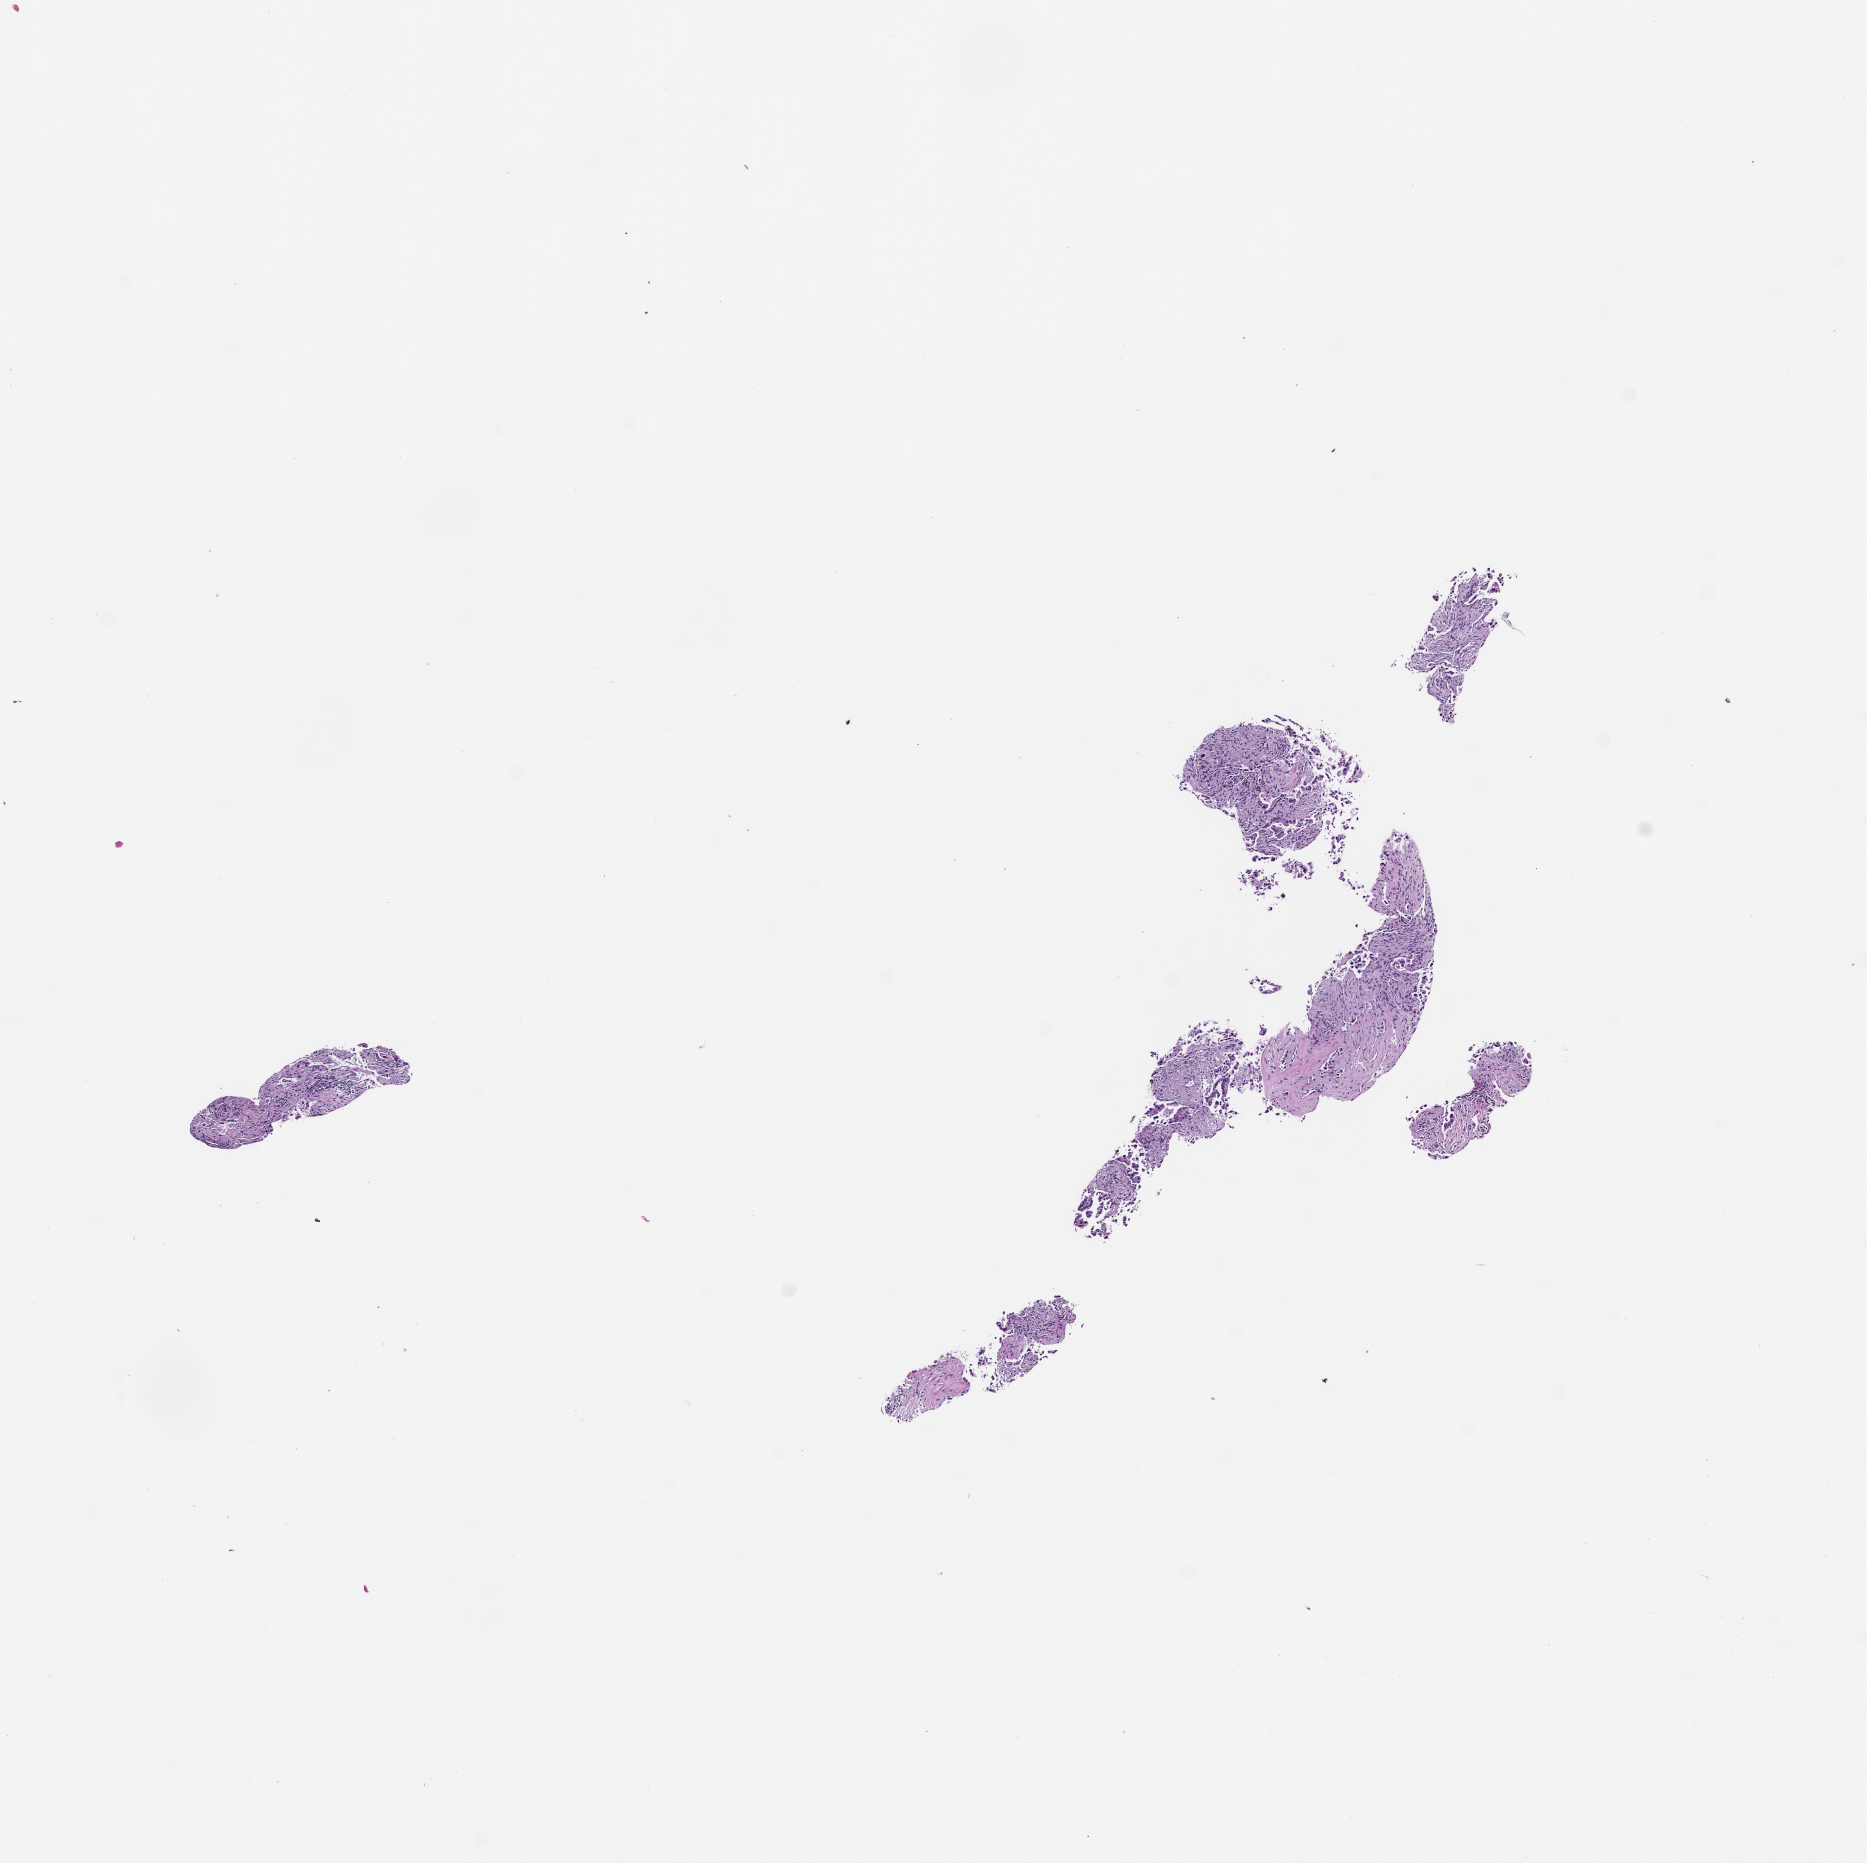
Hematoxylin and eosin (H&E) whole-slide image, whole scanned area (about 7.5 x 7.5 mm) shown as a low-resolution overview, formalin-fixed paraffin-embedded section, site: lung, collected at baseline (before treatment). Female patient.
* this section: primary tumour tissue
* diagnosis: Non-Small Cell Lung Carcinoma